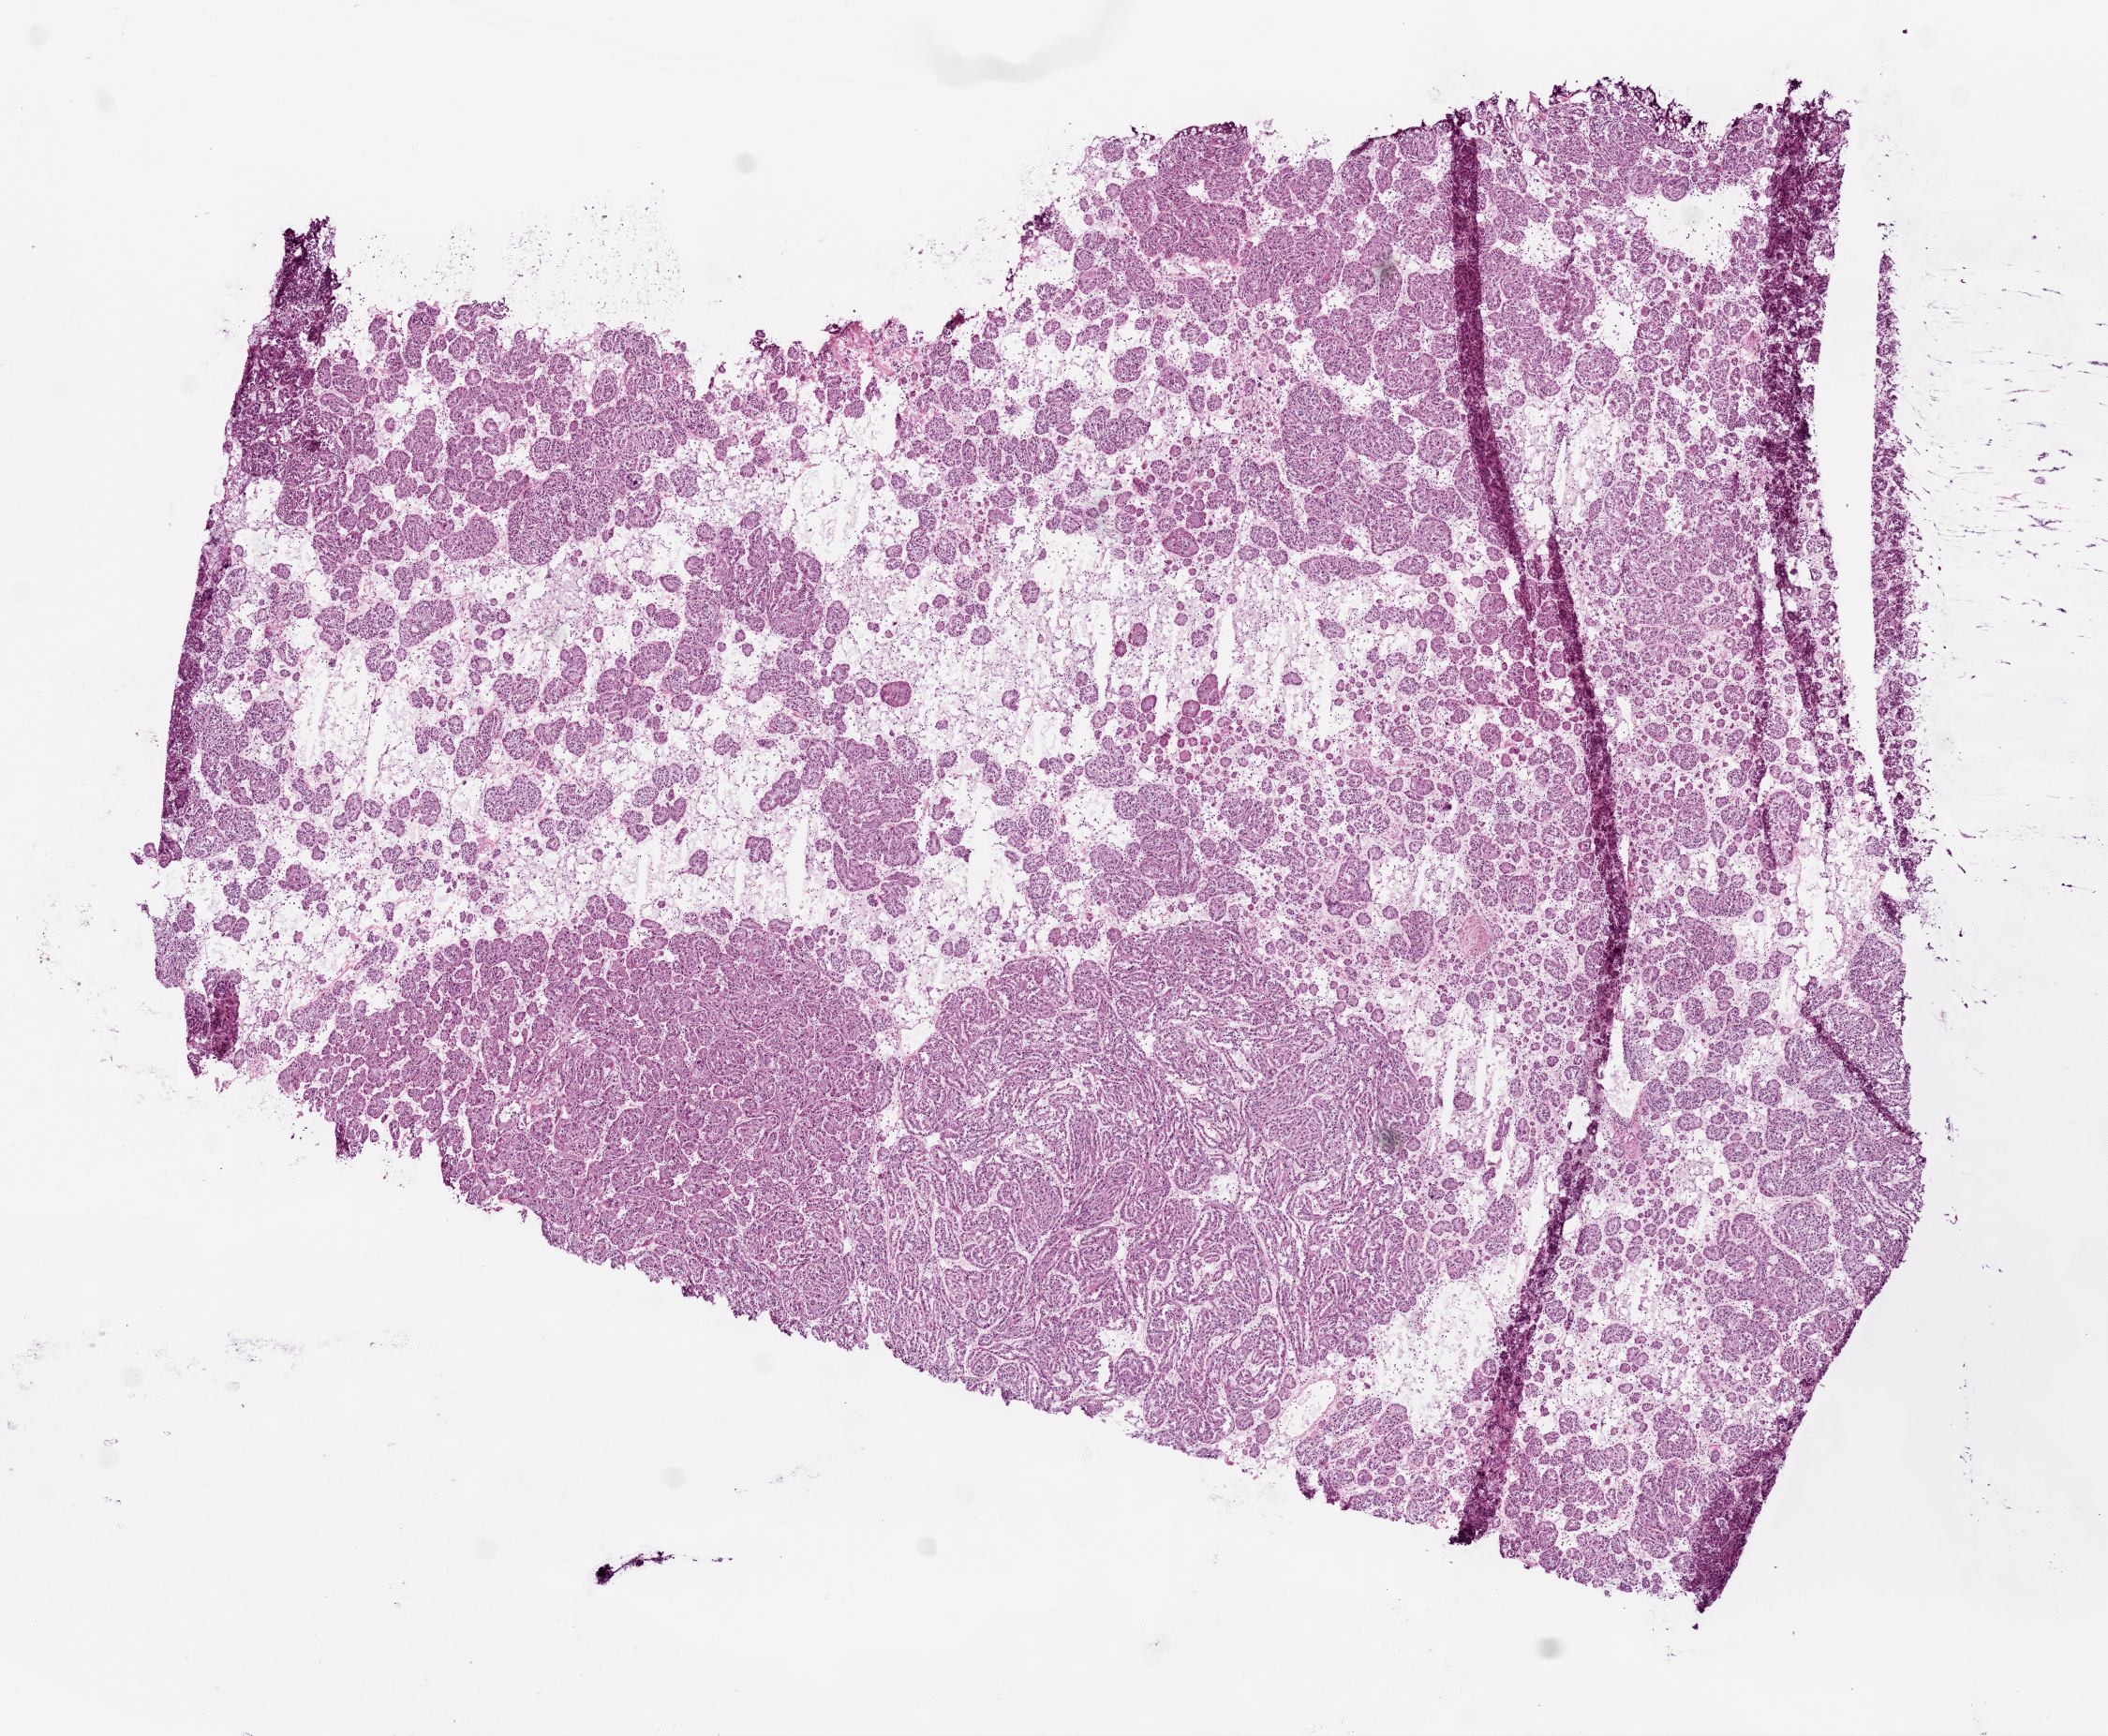
Digitized H&E-stained tissue section (whole slide), low-resolution overview of the scanned area, about 9.0 x 7.4 mm (slide scanned at 20x). Frozen section from the top of the tissue portion. Sample: primary tumour, kidney. Patient: female, age at initial diagnosis 48 years. Pathologist review of this section (percent, as recorded): tumour cells 80%, tumour nuclei 80%, normal cells 0%, stromal cells 20%, necrosis 0%.
Histologic diagnosis: Papillary adenocarcinoma, NOS.